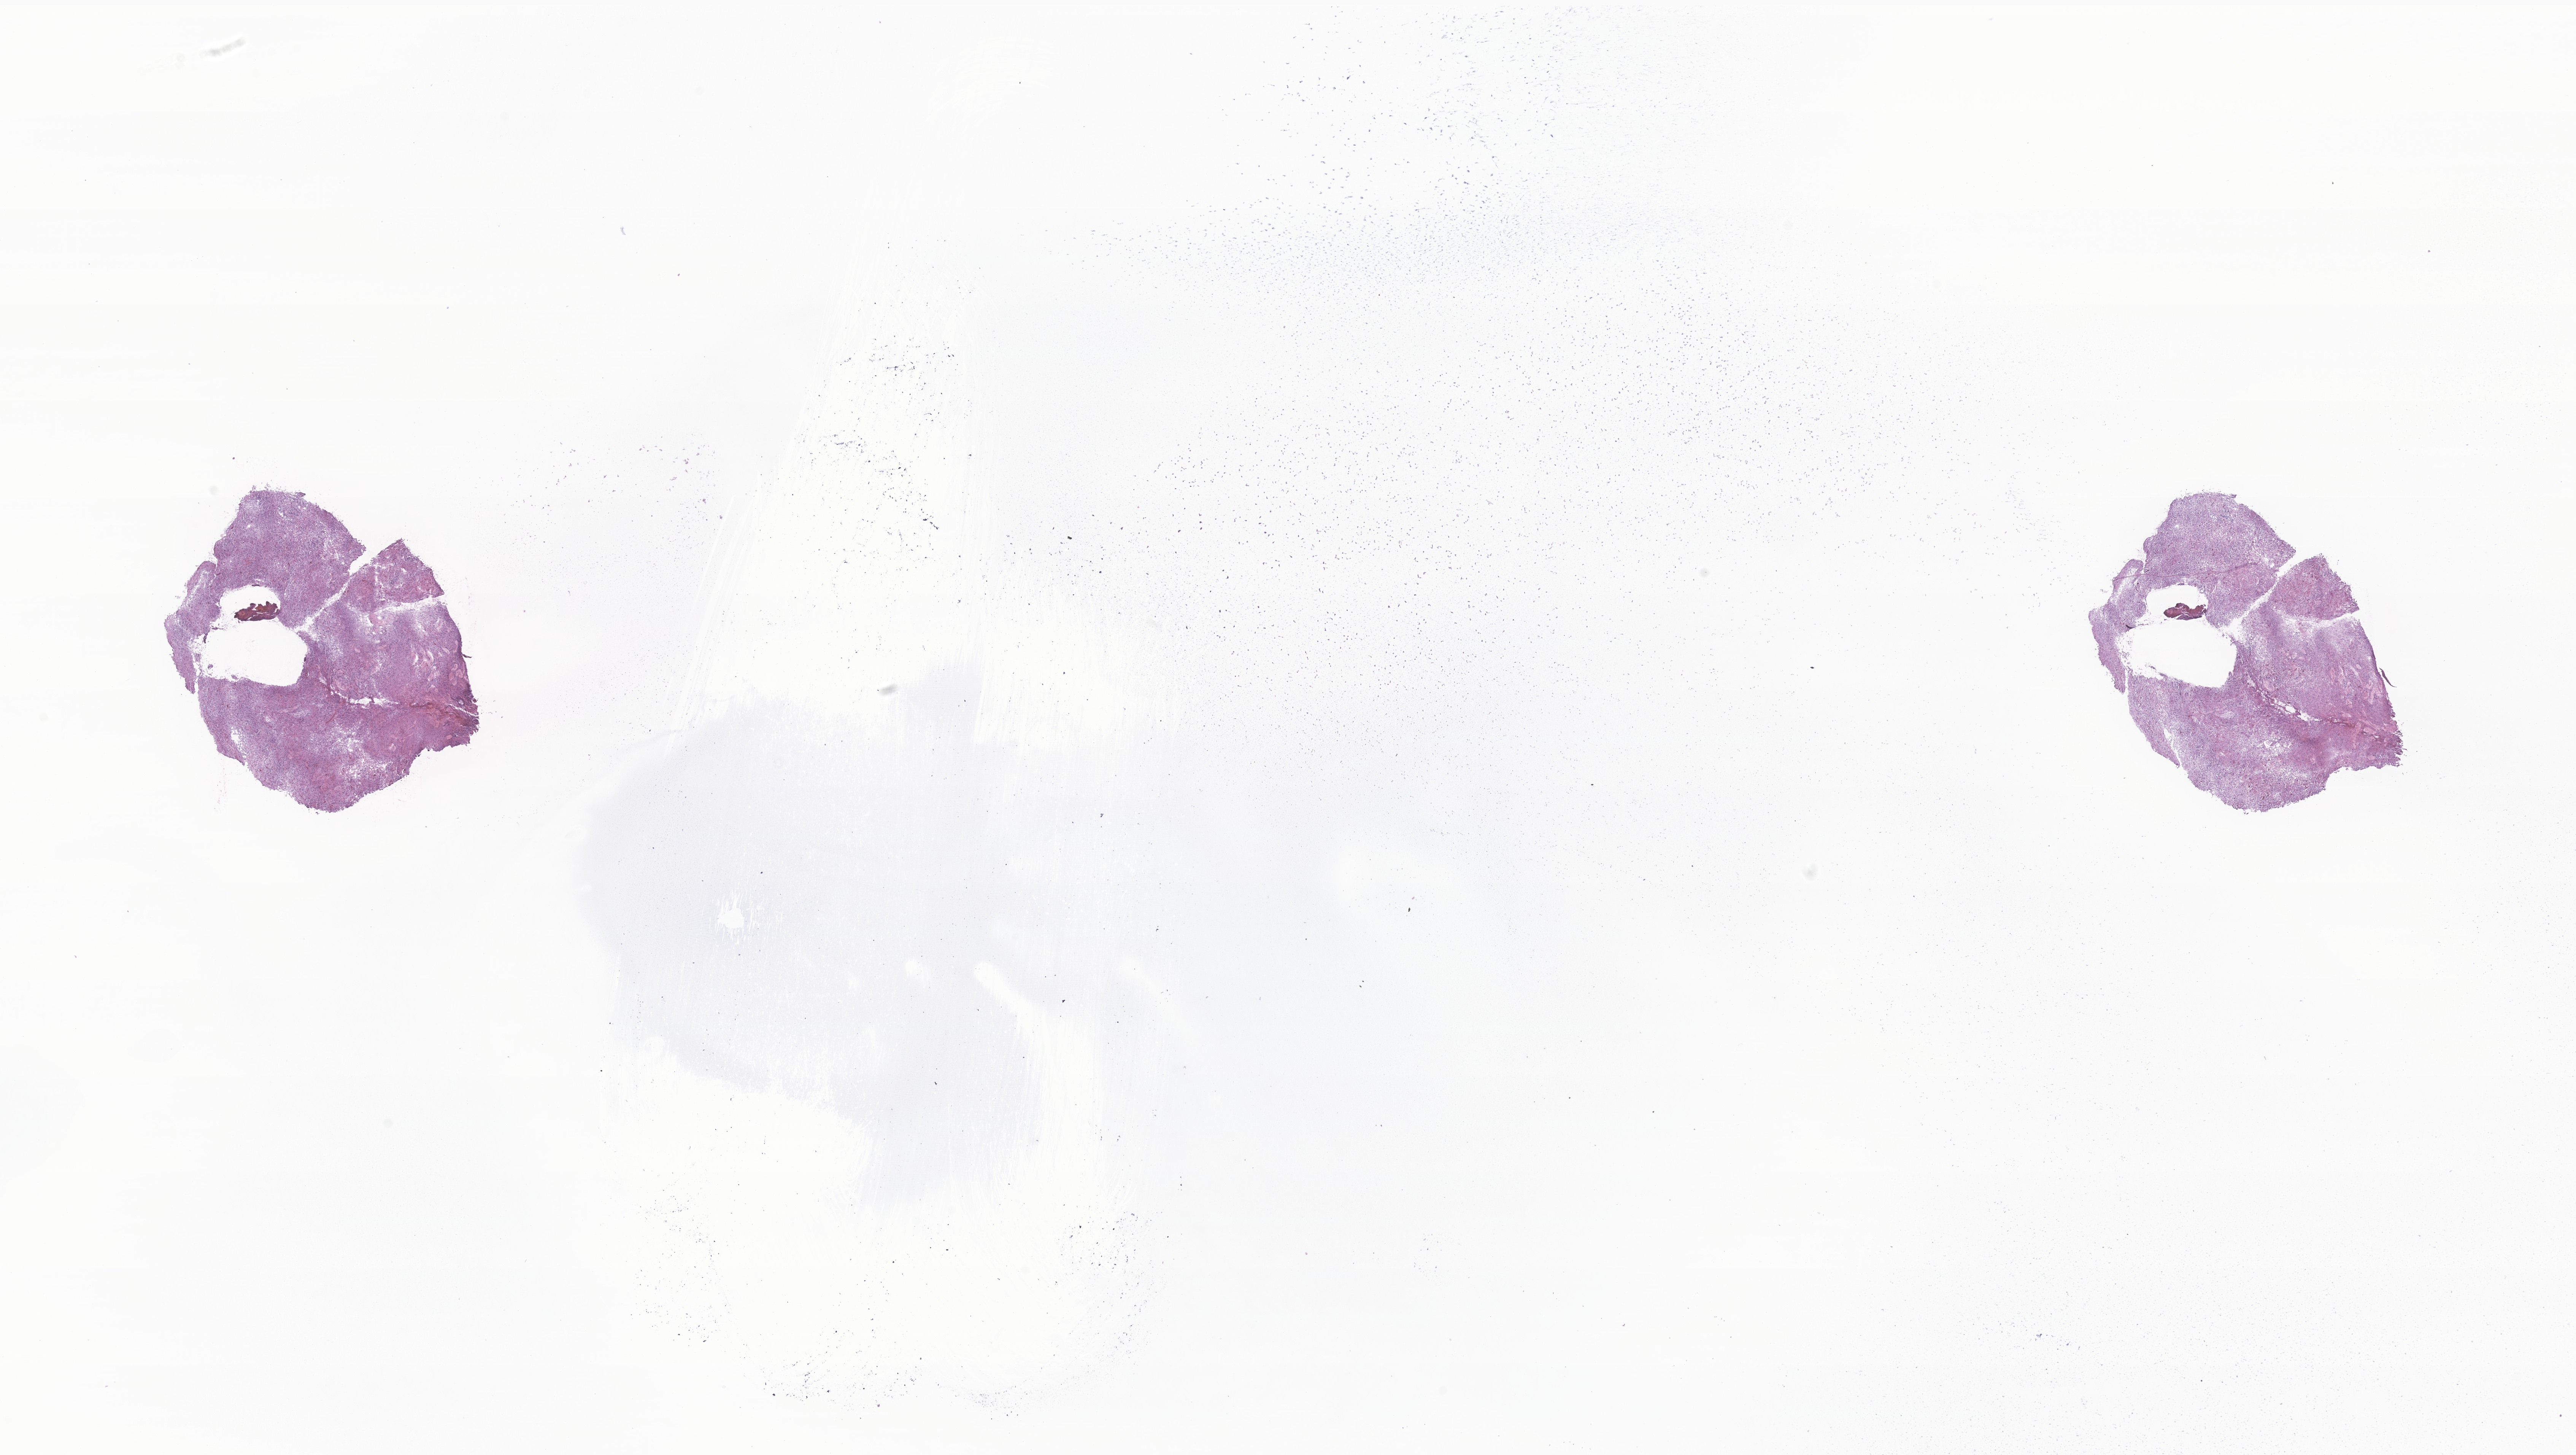
H&E whole-slide image of tumor tissue from the brain, a low-resolution overview of the entire scanned area, about 28.6 x 16.1 mm; frozen section (OCT-embedded). Patient male; age 185 months (15 years 5 months).
Diagnosis (ICD-O-3 morphology term): Pilocytic astrocytoma.